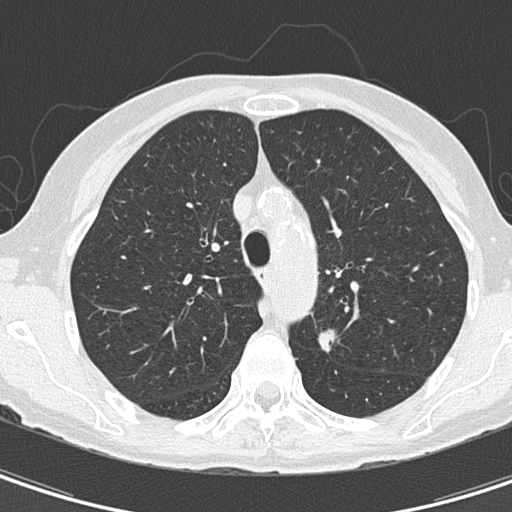
Chest CT (low-dose screening protocol), one axial image. First (baseline) screen. Lung window (W 1500 / L -600 HU). 2 mm slice thickness. Lung (sharp) reconstruction kernel (B50f). Slice 46 of 157 in the series. 512 × 512 image matrix. Female, age 67 years at enrolment. Current smoker at enrolment.
Expert-annotated lung lesion, box from (x=300, y=320) to (x=356, y=366) px. The exam's reader record, not a measurement of the box and not confirmed to be the same lesion: non-calcified nodule or mass ≥4 mm, left upper lobe, 11 × 8 mm, spiculated (stellate) margins, soft tissue attenuation. Official screen result: positive, change unspecified: nodule(s) >= 4 mm or enlarging nodule(s), mass(es), or other non-specific abnormalities suspicious for lung cancer.